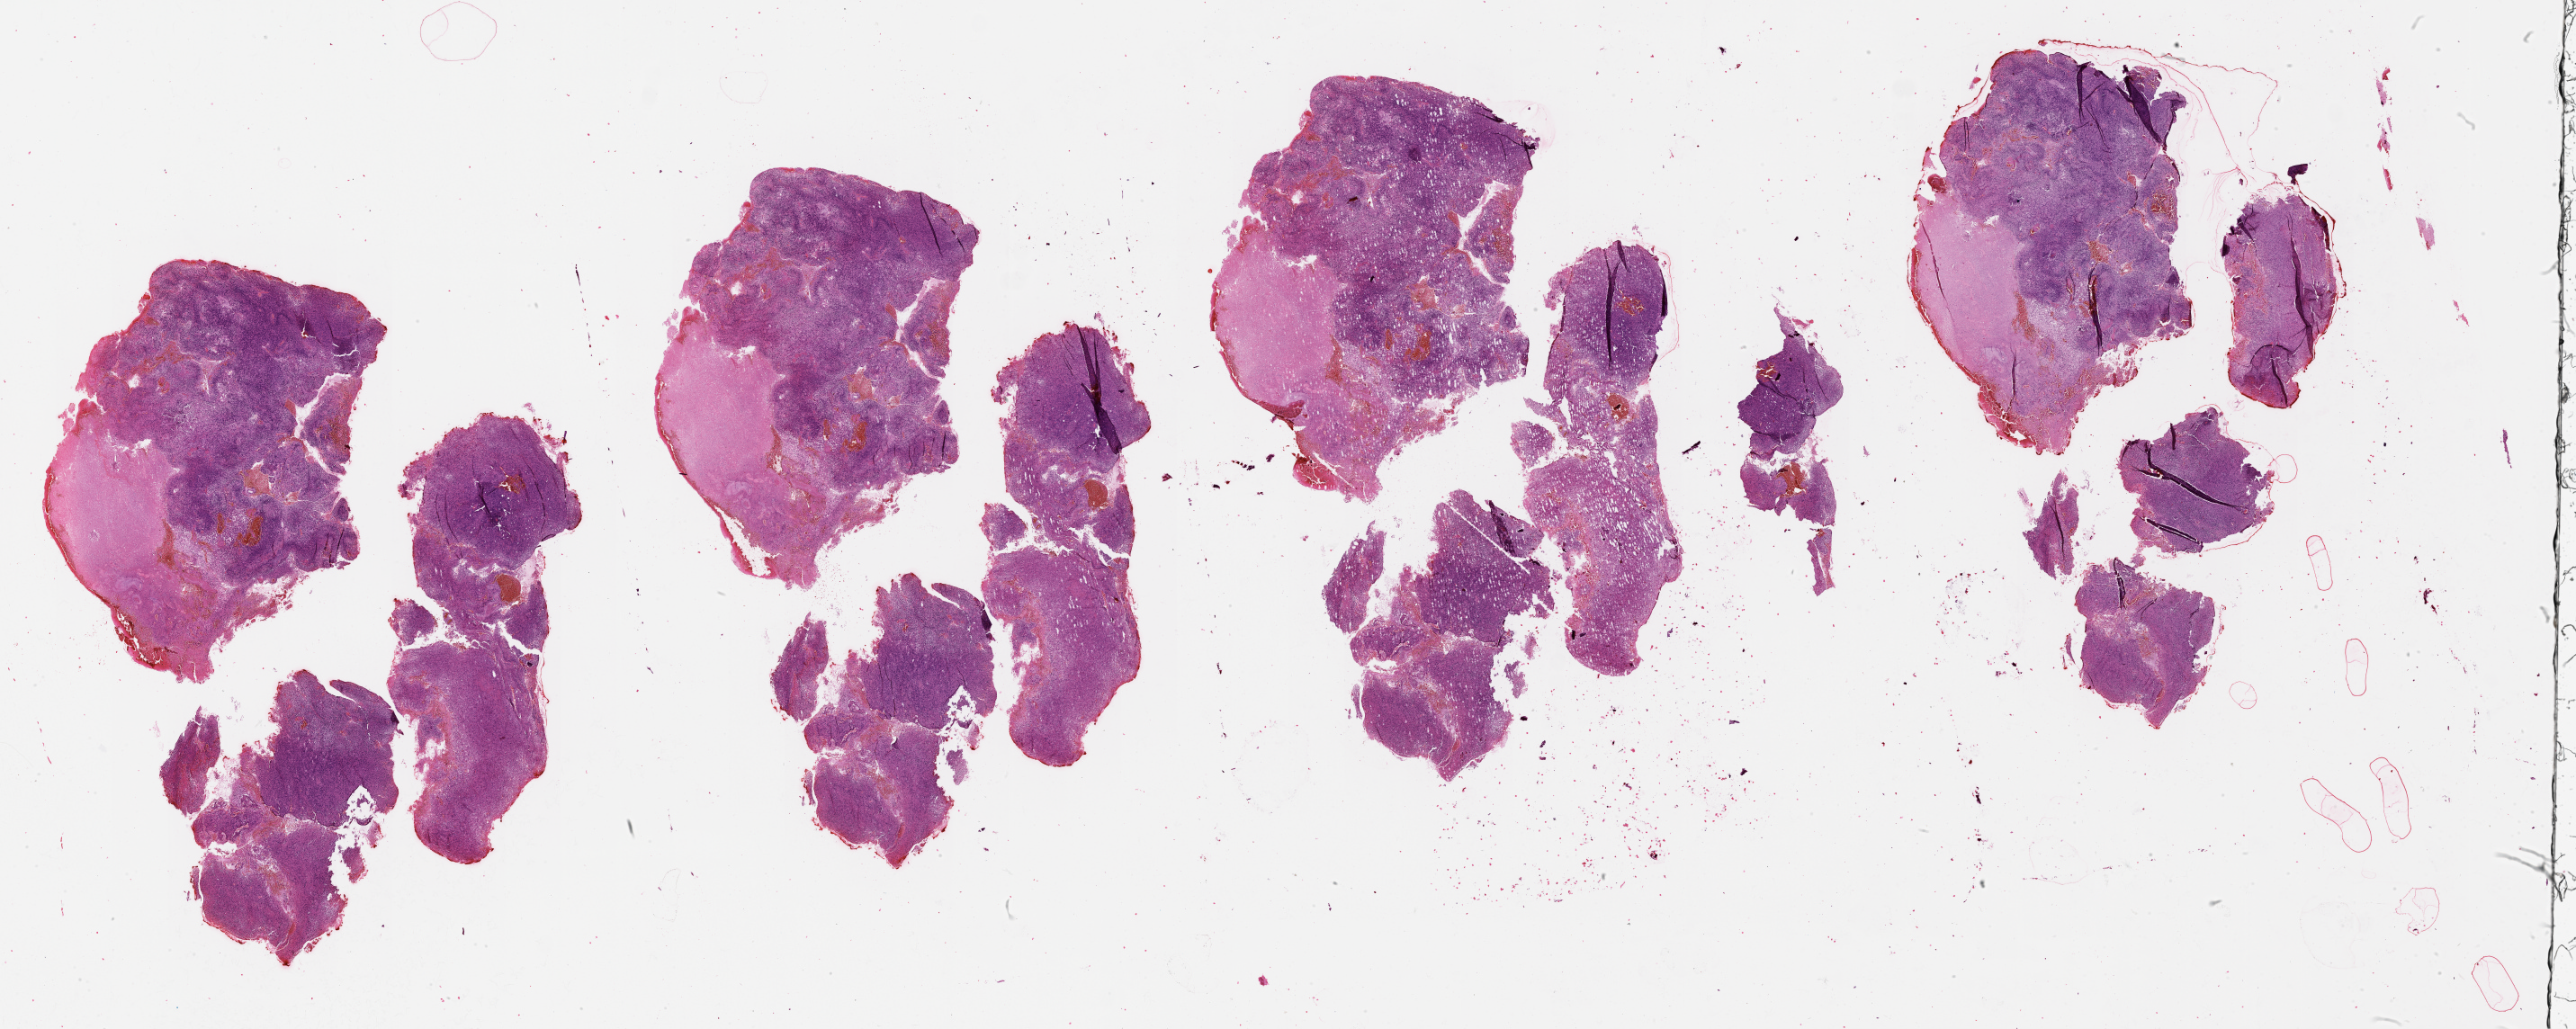
Digitized H&E tissue section (whole slide) — shown as a low-resolution overview of the whole scanned area (about 46.1 x 18.4 mm, slide scanned at 20x); brain, tumour tissue. 37-year-old female patient.
Diagnosis: Glioblastoma. Primary tumour site (as recorded): occipital lobe.